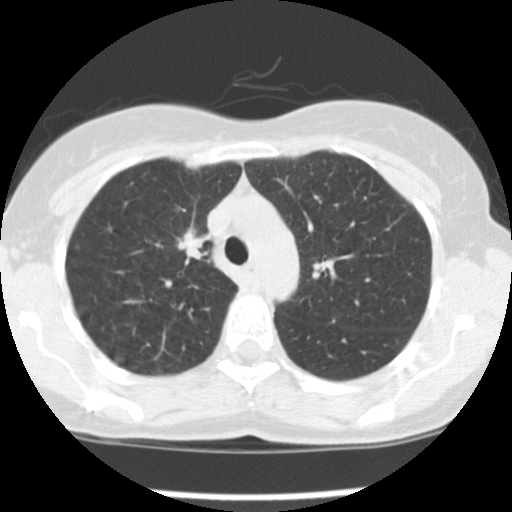
Chest CT (low-dose screening protocol), one axial image; first (baseline) screen; lung window (W 1500 / L -600 HU); slice 114 of 157 in the series. Female participant, aged 57 years at enrolment. Current smoker at enrolment.
- Expert reader's lesion annotation, box from (x=166, y=226) to (x=216, y=270) px.
- The exam's reader record, not a measurement of the box and not confirmed to be the same lesion: non-calcified nodule or mass ≥4 mm, left upper lobe, 7 × 6 mm, poorly defined margins, ground glass attenuation.
- Note: the box lies in the patient's right hemithorax on this image, whereas the reader's record names the left lung; they may be different findings.
- Later outcome: lung cancer diagnosed 15 days after this screen — adenocarcinoma, NOS, right upper lobe, moderately differentiated (G2), stage IA (AJCC 6th edition), 15 mm at pathology.